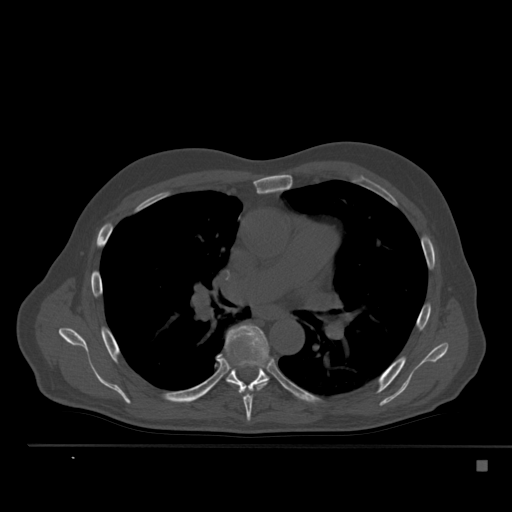
CT including the spine, one axial slice; position 338 of 517 along the scan axis; reconstruction kernel Br40s; 120 kVp; bone window (W 1800 / L 400 HU); 512 × 512 image matrix, field of view 408 × 408 mm. Patient: male, 70 years. From the clinical record (not read from this slice): primary cancer: renal.
Structures marked on this image (semi-automatic segmentation, software-assisted and operator-edited):
- T6 vertebra: bounding box (x1, y1, x2, y2) in pixels: (225, 324, 270, 422)
- T7 vertebra: (205, 364, 269, 394)